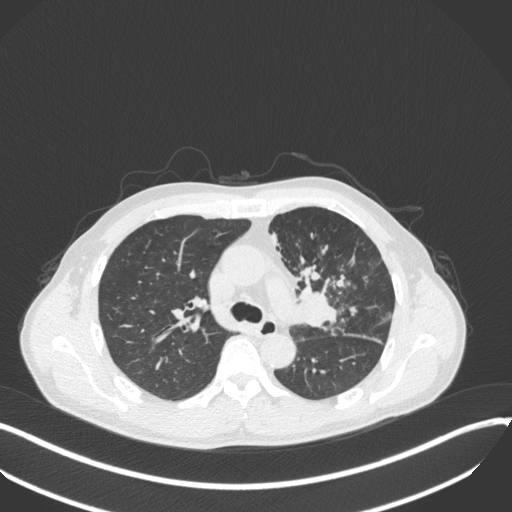
Chest CT, one axial slice; slice 225 of 411 in the series (ordered by position); lung window (W 1500 / L -600 HU); 512 × 512 image matrix, field of view 400 × 400 mm. Patient: male, 56 years. Case-level facts recorded for this patient, not image findings: clinical TNM (as recorded): T2a N0 M0.
Outlined on this slice (rectangle marked by the reading radiologist):
- lung tumour (recorded histology: squamous cell carcinoma): box from (x=294, y=271) to (x=341, y=334) px